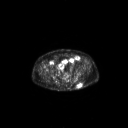
FDG PET of an extremity soft-tissue mass (from a PET/CT study), one axial slice. Slice 73 of 267 in the series (ordered by position). 128 × 128 image matrix. Patient: male, 69 years. From the clinical record (not read from this slice): histological type: leiomyosarcoma; grade: intermediate; site of the primary tumour: left pelvis.
Annotated regions visible in this slice (expert contour drawn on MRI and transferred to this co-registered scan by the dataset authors):
- gross tumour volume (mass): bounding box <77,84,82,88> (left, top, right, bottom; pixels)